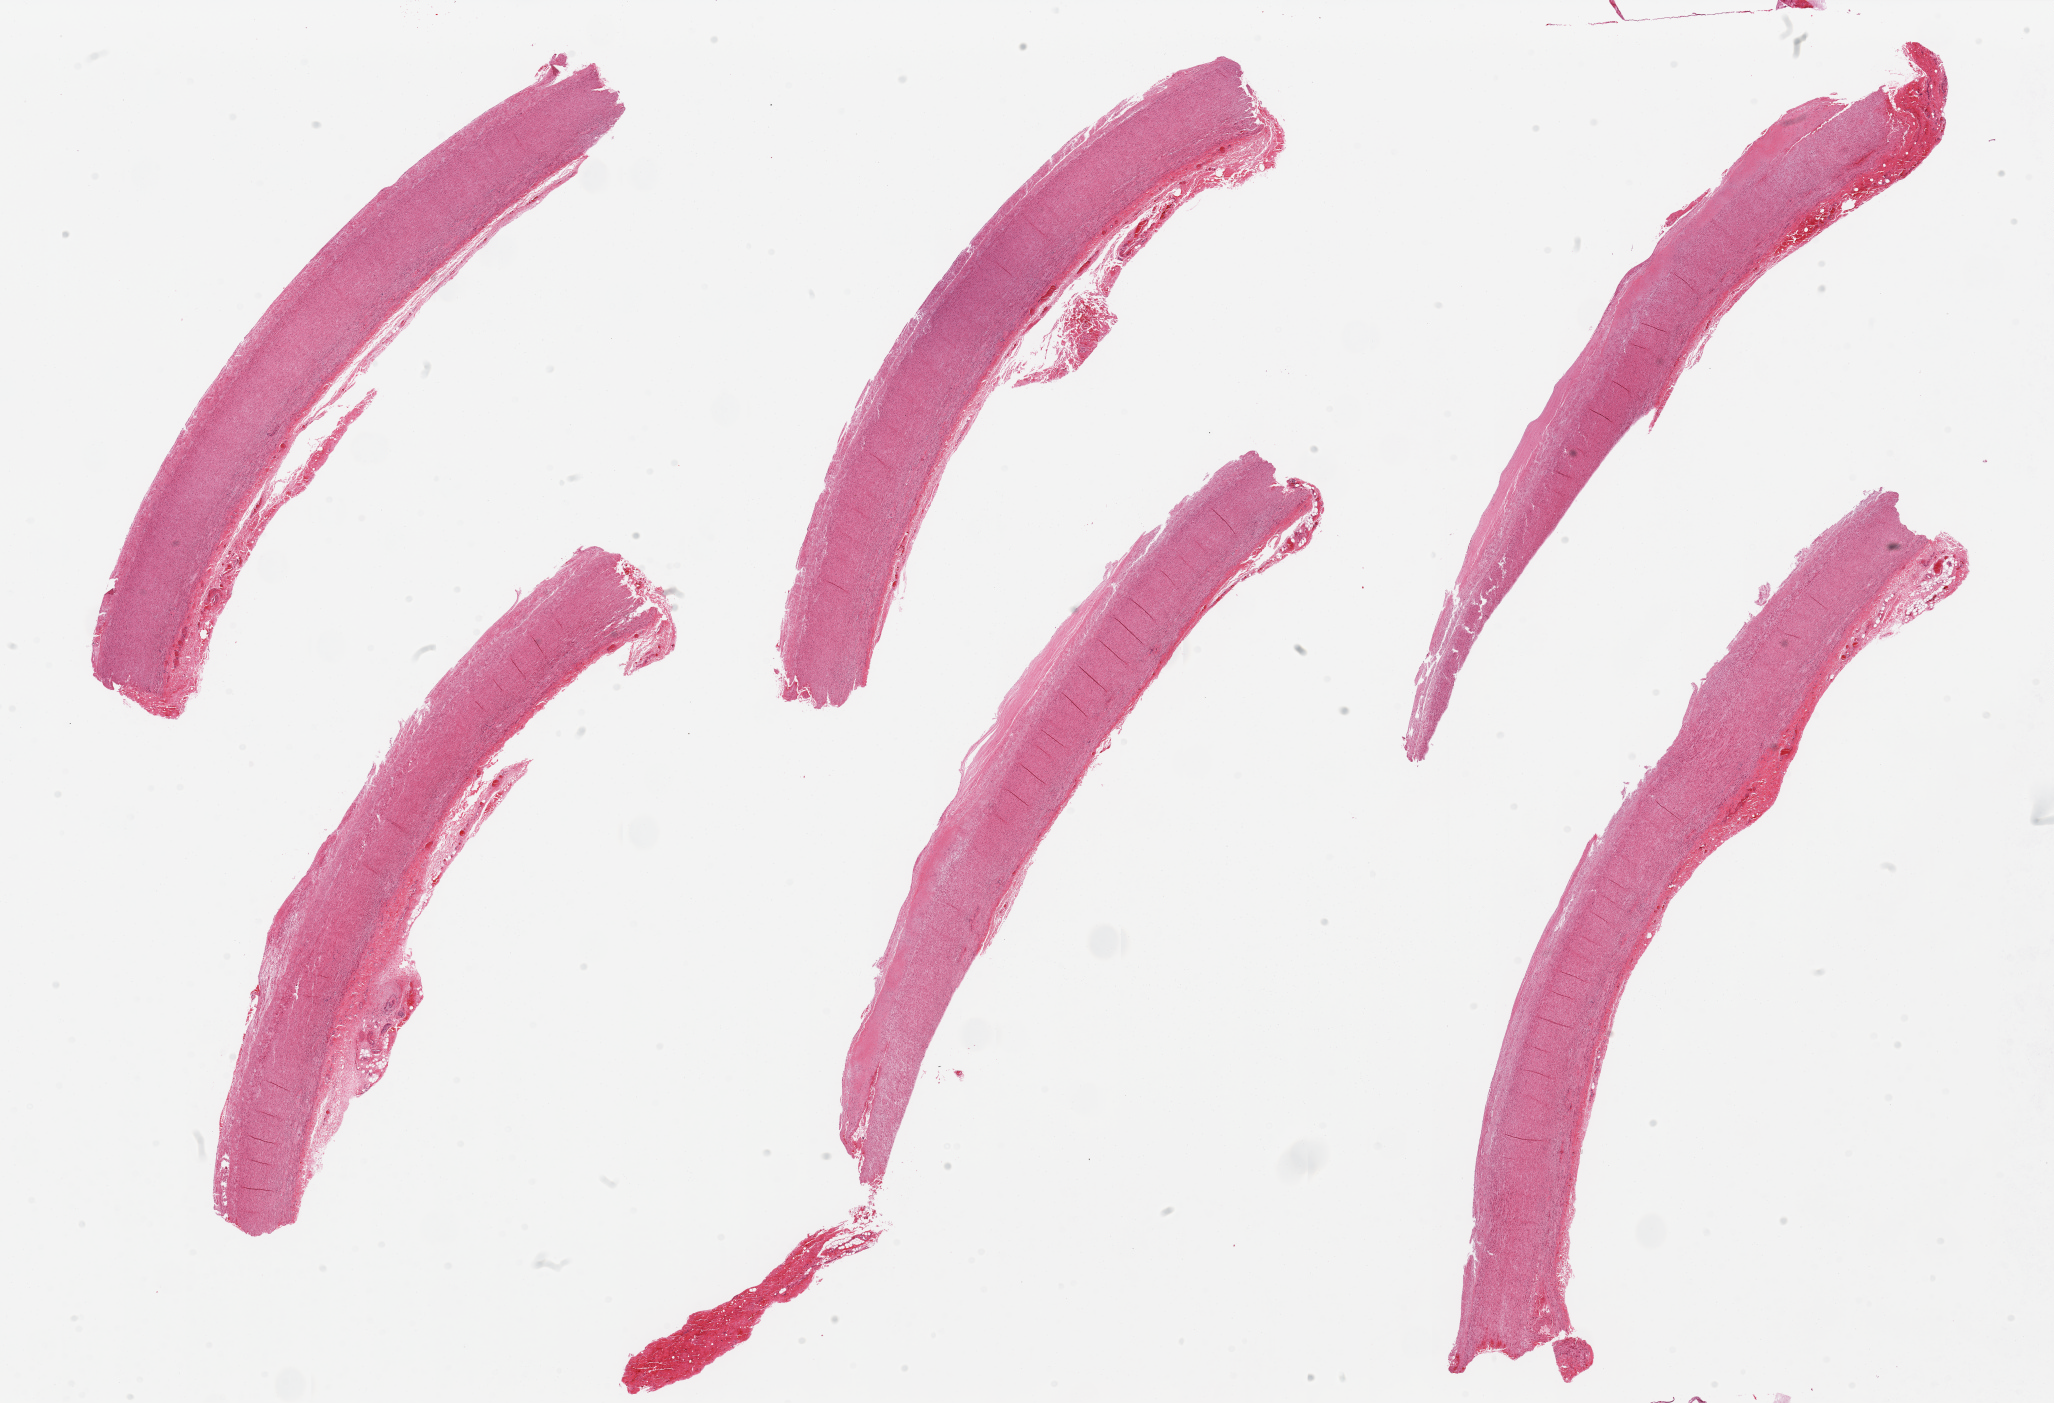
Whole-slide image, hematoxylin and eosin (H&E) stain, a low-resolution overview of the entire scanned area, about 32.5 x 22.2 mm (slide scanned at 20x). PAXgene-fixed paraffin-embedded (PFPE) section. Target tissue: aorta. Tissue donor sample. Donor sex: female.
Pathologist's review note for this sample: 6 pieces.